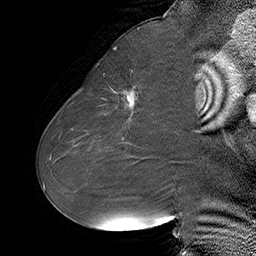
Breast MRI (dynamic contrast-enhanced), one sagittal slice; slice 29 of 55 in the series (ordered by position); dynamic contrast-enhanced series, time point 2 of 6 at this slice position (early post-contrast); 1.5 T; TE 4.5 ms, TR 32.4 ms; 256 × 256 image matrix, field of view 180 × 180 mm. Female patient. From the clinical record (not read from this slice): setting: breast cancer imaged before/during neoadjuvant chemotherapy; receptor status: HER2-positive.
Outlined on this slice (semi-automatically segmented with operator editing):
- analysis volume of interest (the breast-tissue region the enhancement analysis was run in; not a lesion): bounding box <80,64,163,134> (left, top, right, bottom; pixels)
- tumour enhancement mask (voxels above the 100 % enhancement threshold inside the analysis volume of interest): <114,88,134,110>